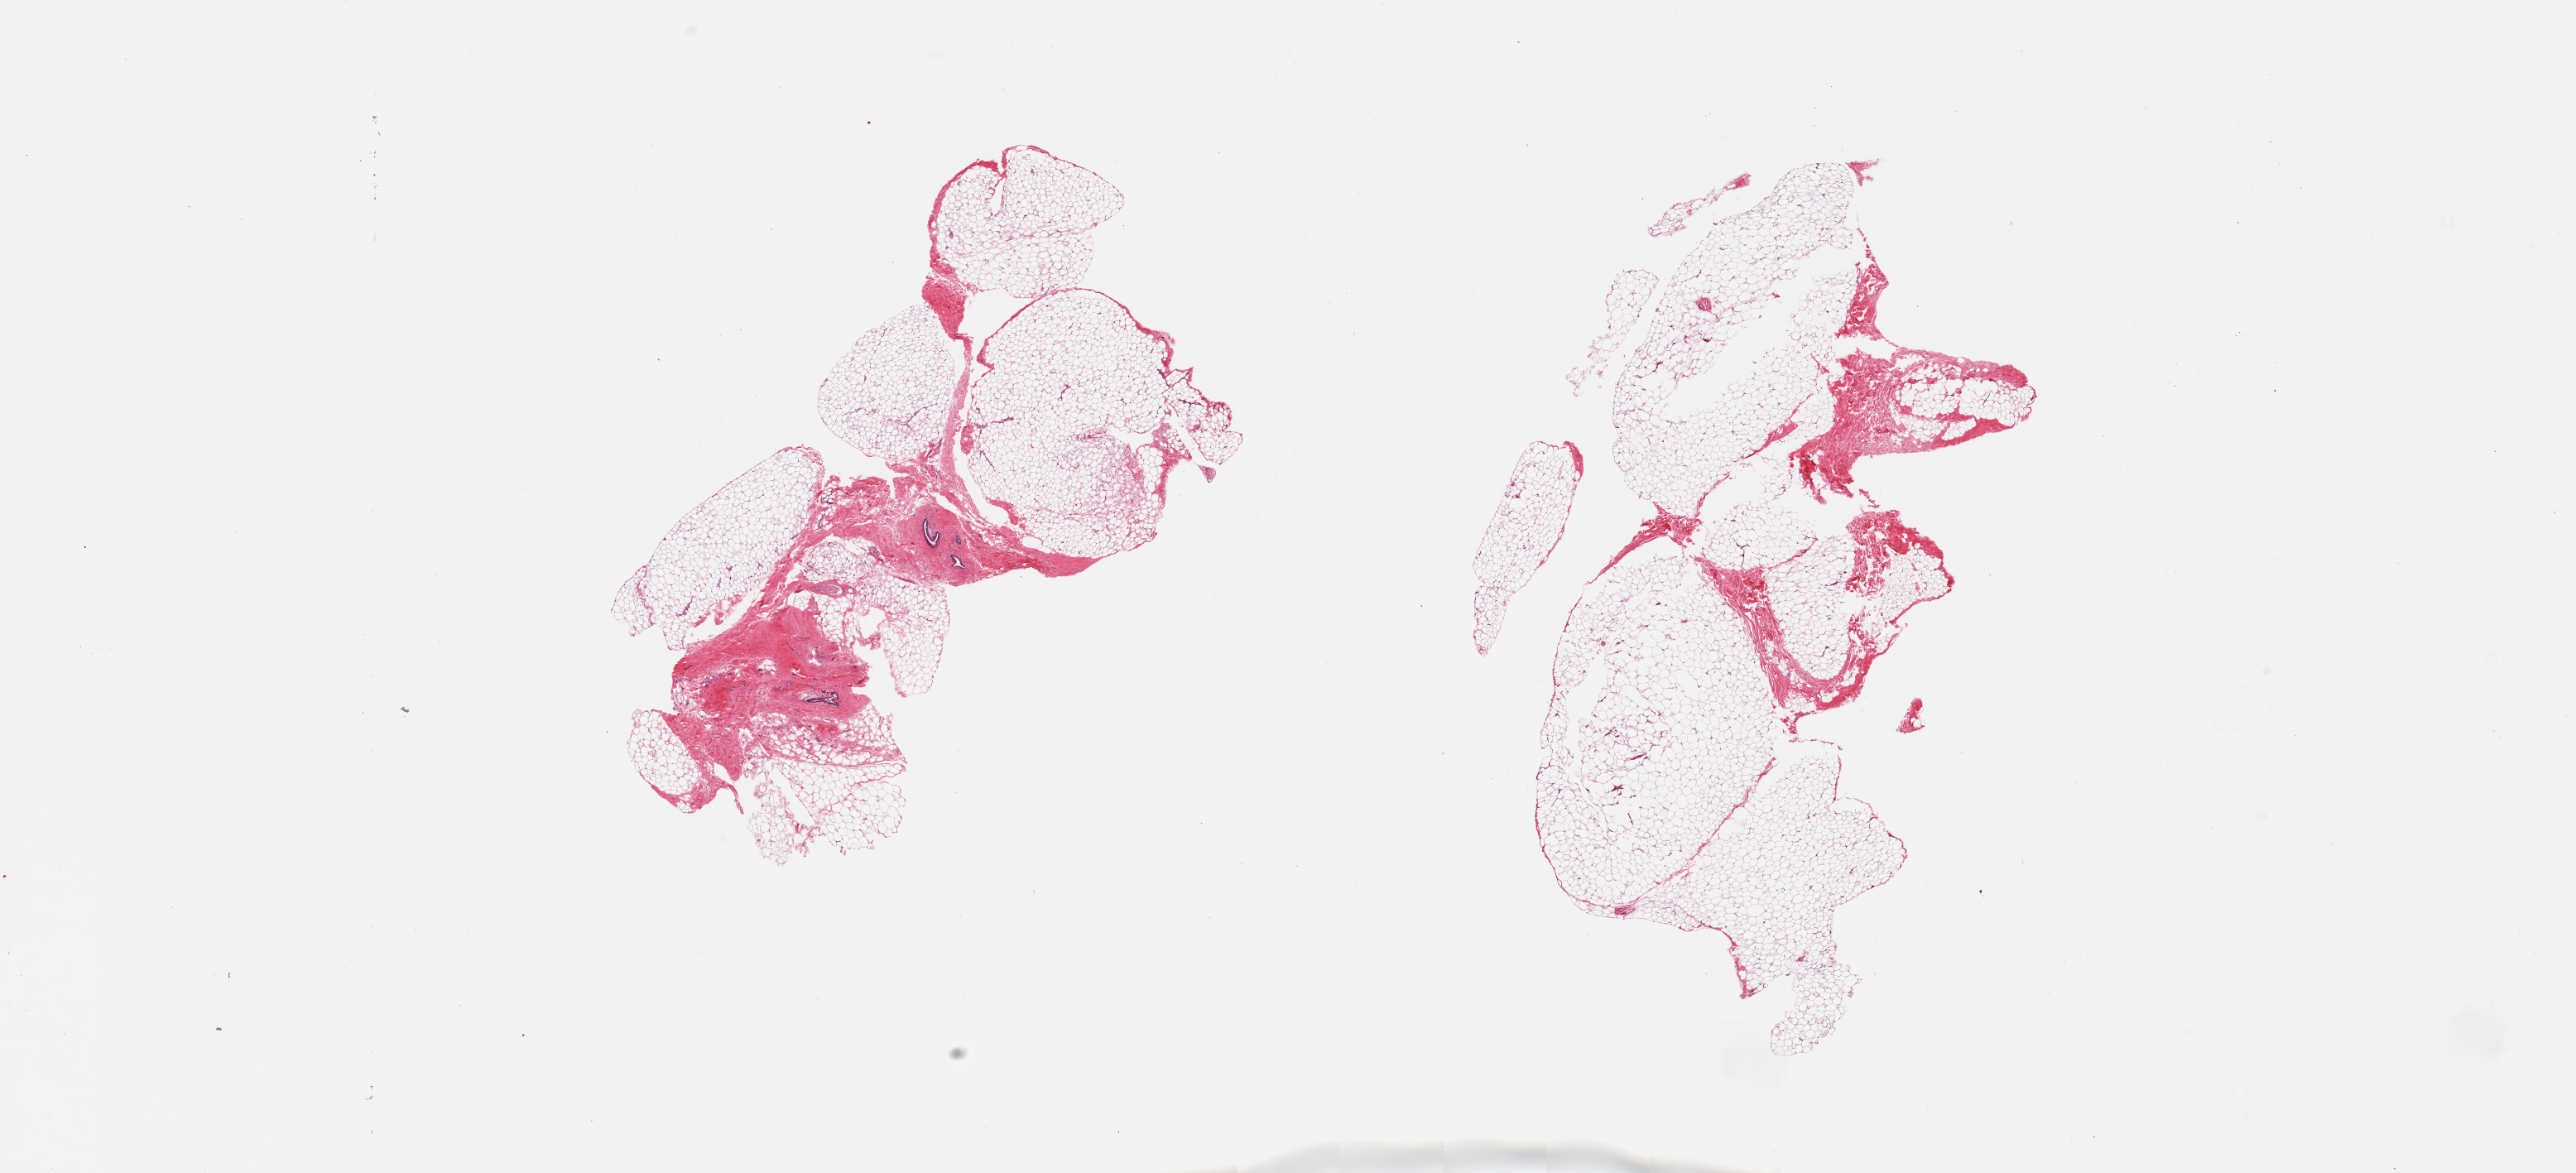
H&E whole-slide image, brightfield — whole scanned area (about 24.6 x 11.2 mm, slide scanned at 20x) shown as a low-resolution overview. PAXgene-fixed, paraffin-embedded tissue. Target tissue: breast. Donor tissue sample. Male donor.
• pathologist's review note for this sample: 2 pieces; predominantly fat with 15 and 25% fibrous stroma with few ducts